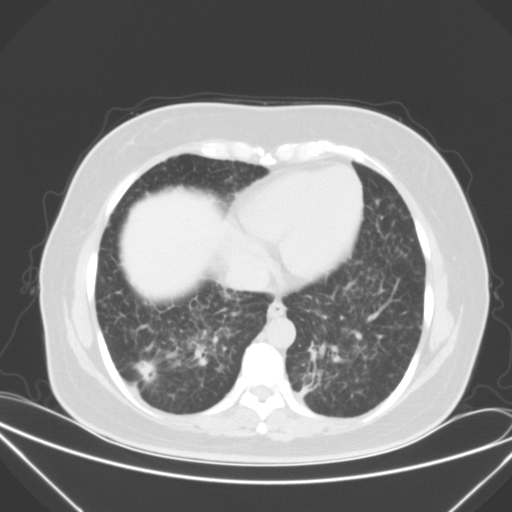
Chest CT, one axial slice; position 16 of 52 along the scan axis; lung window (W 1500 / L -600 HU); 5 mm slice thickness; 512 × 512 image matrix. Female patient, age 50 years. From the clinical record (not read from this slice): clinical TNM (as recorded): T1c N0 M1a.
Structures marked on this image (rectangle marked by the reading radiologist):
- lung tumour (recorded histology: adenocarcinoma): box from (x=134, y=356) to (x=164, y=398) px